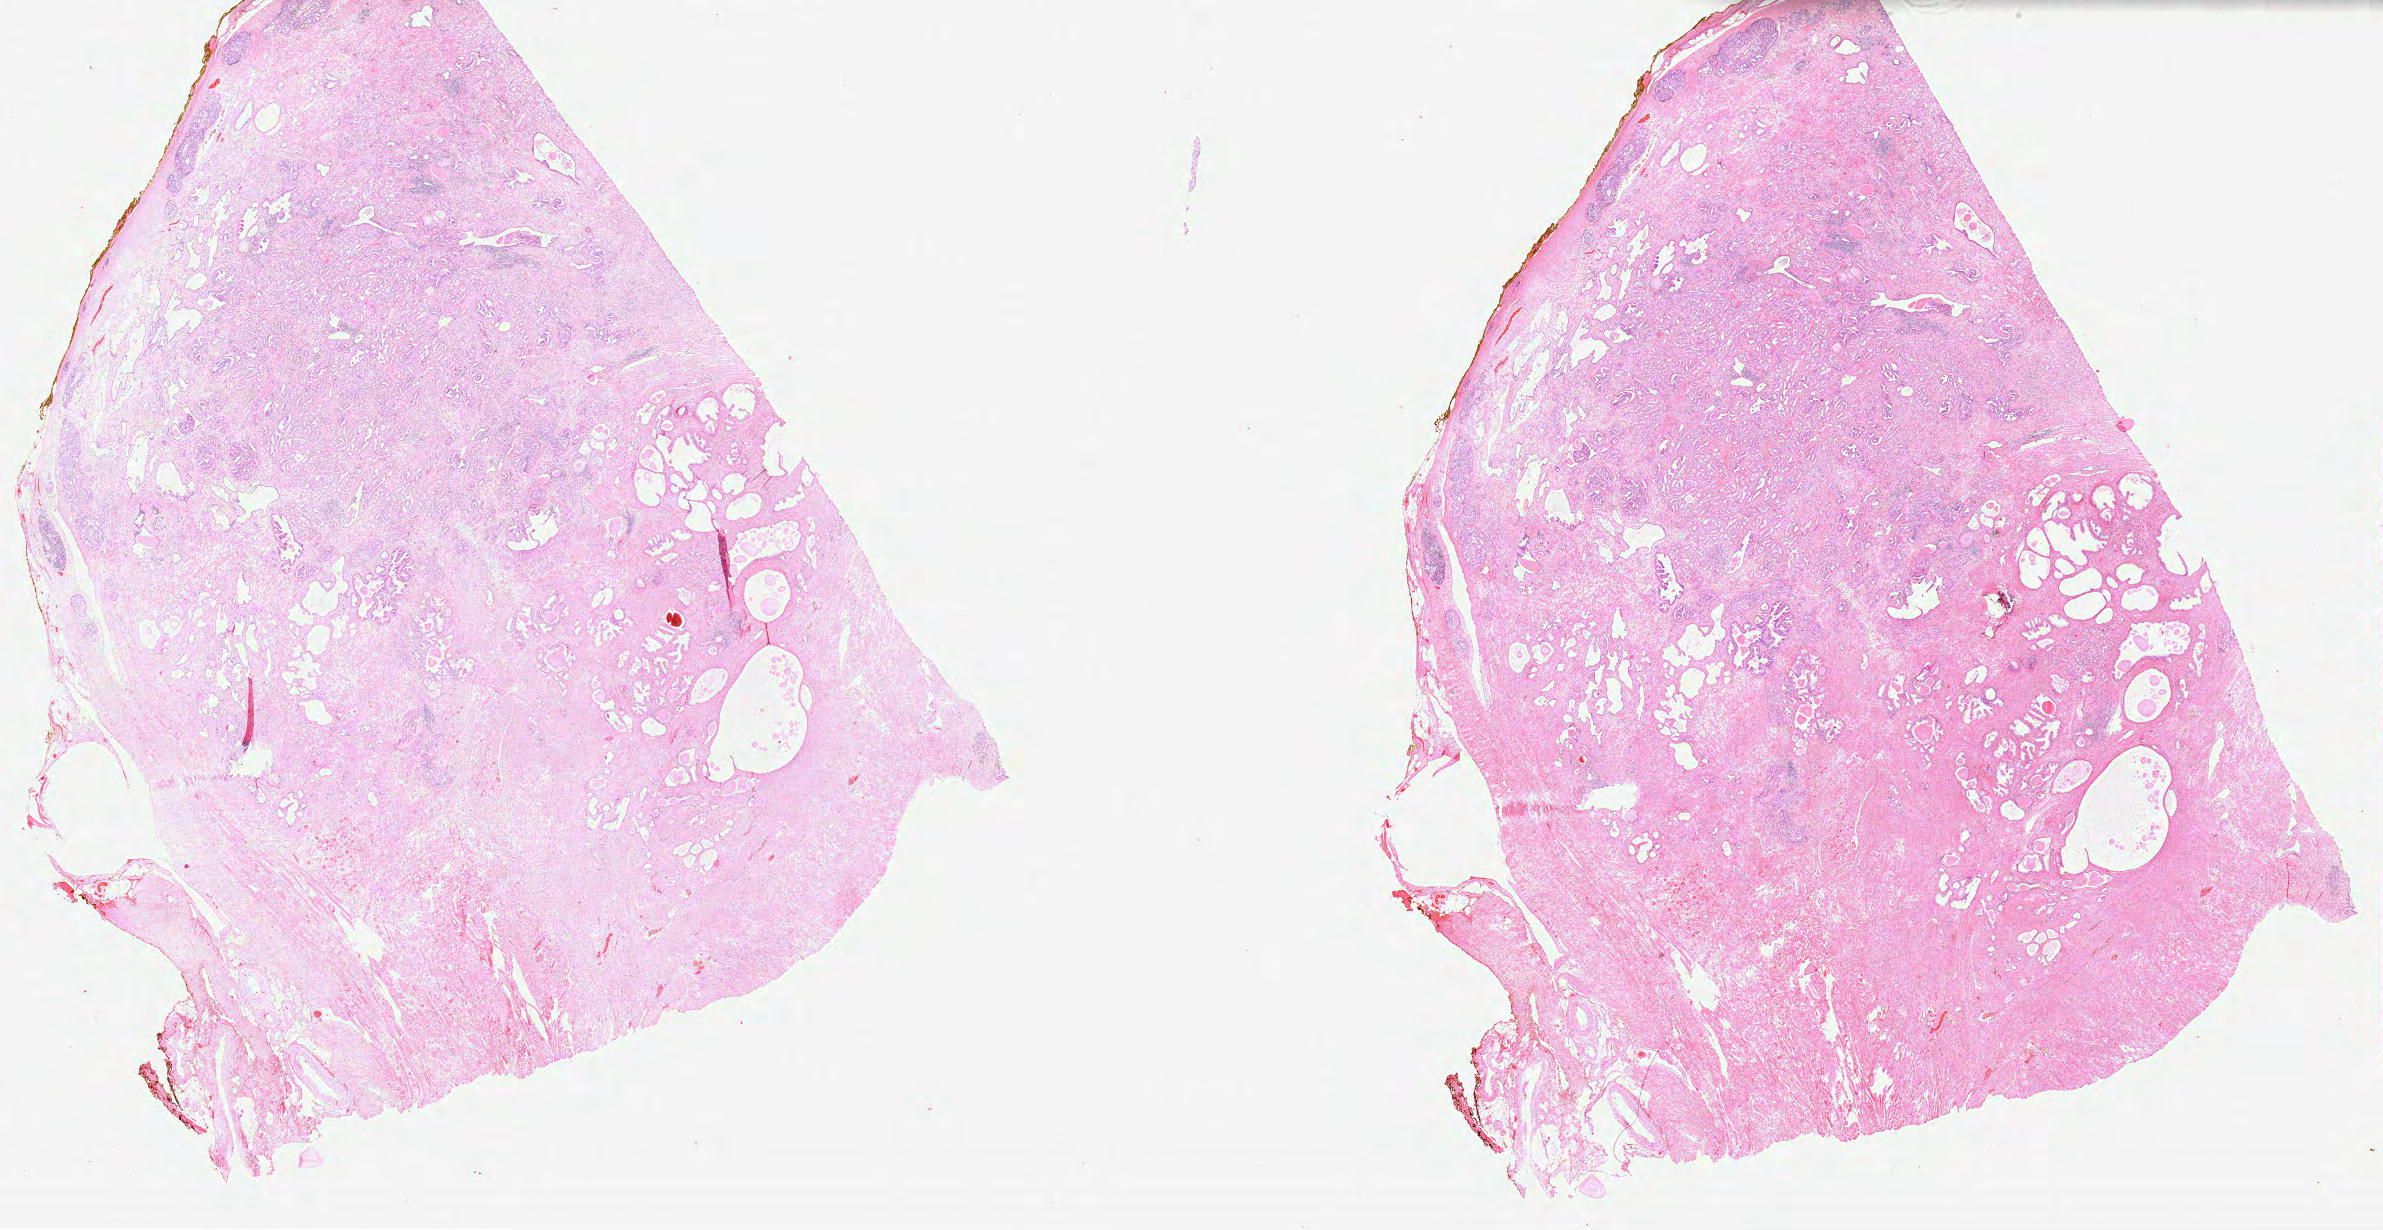
Whole-slide histology image, H&E — low-resolution overview of the scanned area, about 38.4 x 19.8 mm (acquisition: 40x scan), FFPE section, sample: primary tumour, prostate. Patient: male, age at initial diagnosis 61 years. Gleason score: 7 (3+4).
Histologic diagnosis: Acinar cell carcinoma. Lymph nodes positive (case pathology): 0 of 12 examined.